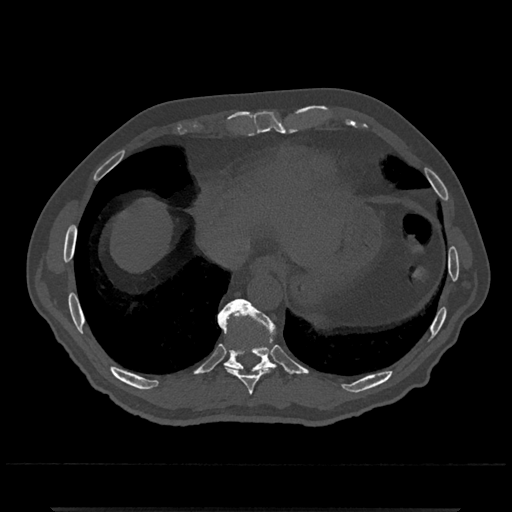
CT including the spine, one axial slice; reconstruction kernel Br40s/3; 120 kVp; bone window (W 1800 / L 400 HU); 512 × 512 image matrix, field of view 393 × 393 mm. Patient: male, 67 years. Case-level facts recorded for this patient, not image findings: primary cancer: prostate.
Annotated regions visible in this slice (semi-automatic segmentation, software-assisted and operator-edited):
- T10 vertebra: bounding box <219,299,276,373> (left, top, right, bottom; pixels)
- T9 vertebra: <219,322,268,395>